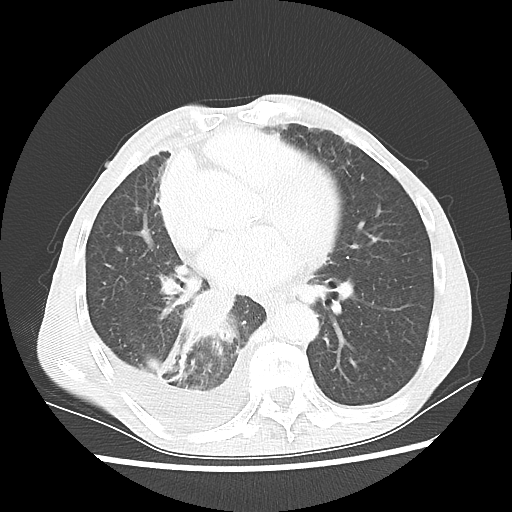
Chest CT, one axial slice; position 27 of 60 along the scan axis; reconstruction kernel LUNG; lung window (W 1500 / L -600 HU); 512 × 512 image matrix. Patient: male, 76 years. From the clinical record (not read from this slice): clinical TNM (as recorded): T3 N3 M1a; histopathological grade: G3.
Outlined on this slice (rectangle marked by the reading radiologist):
- lung tumour (recorded histology: squamous cell carcinoma): box from (x=149, y=288) to (x=239, y=384) px